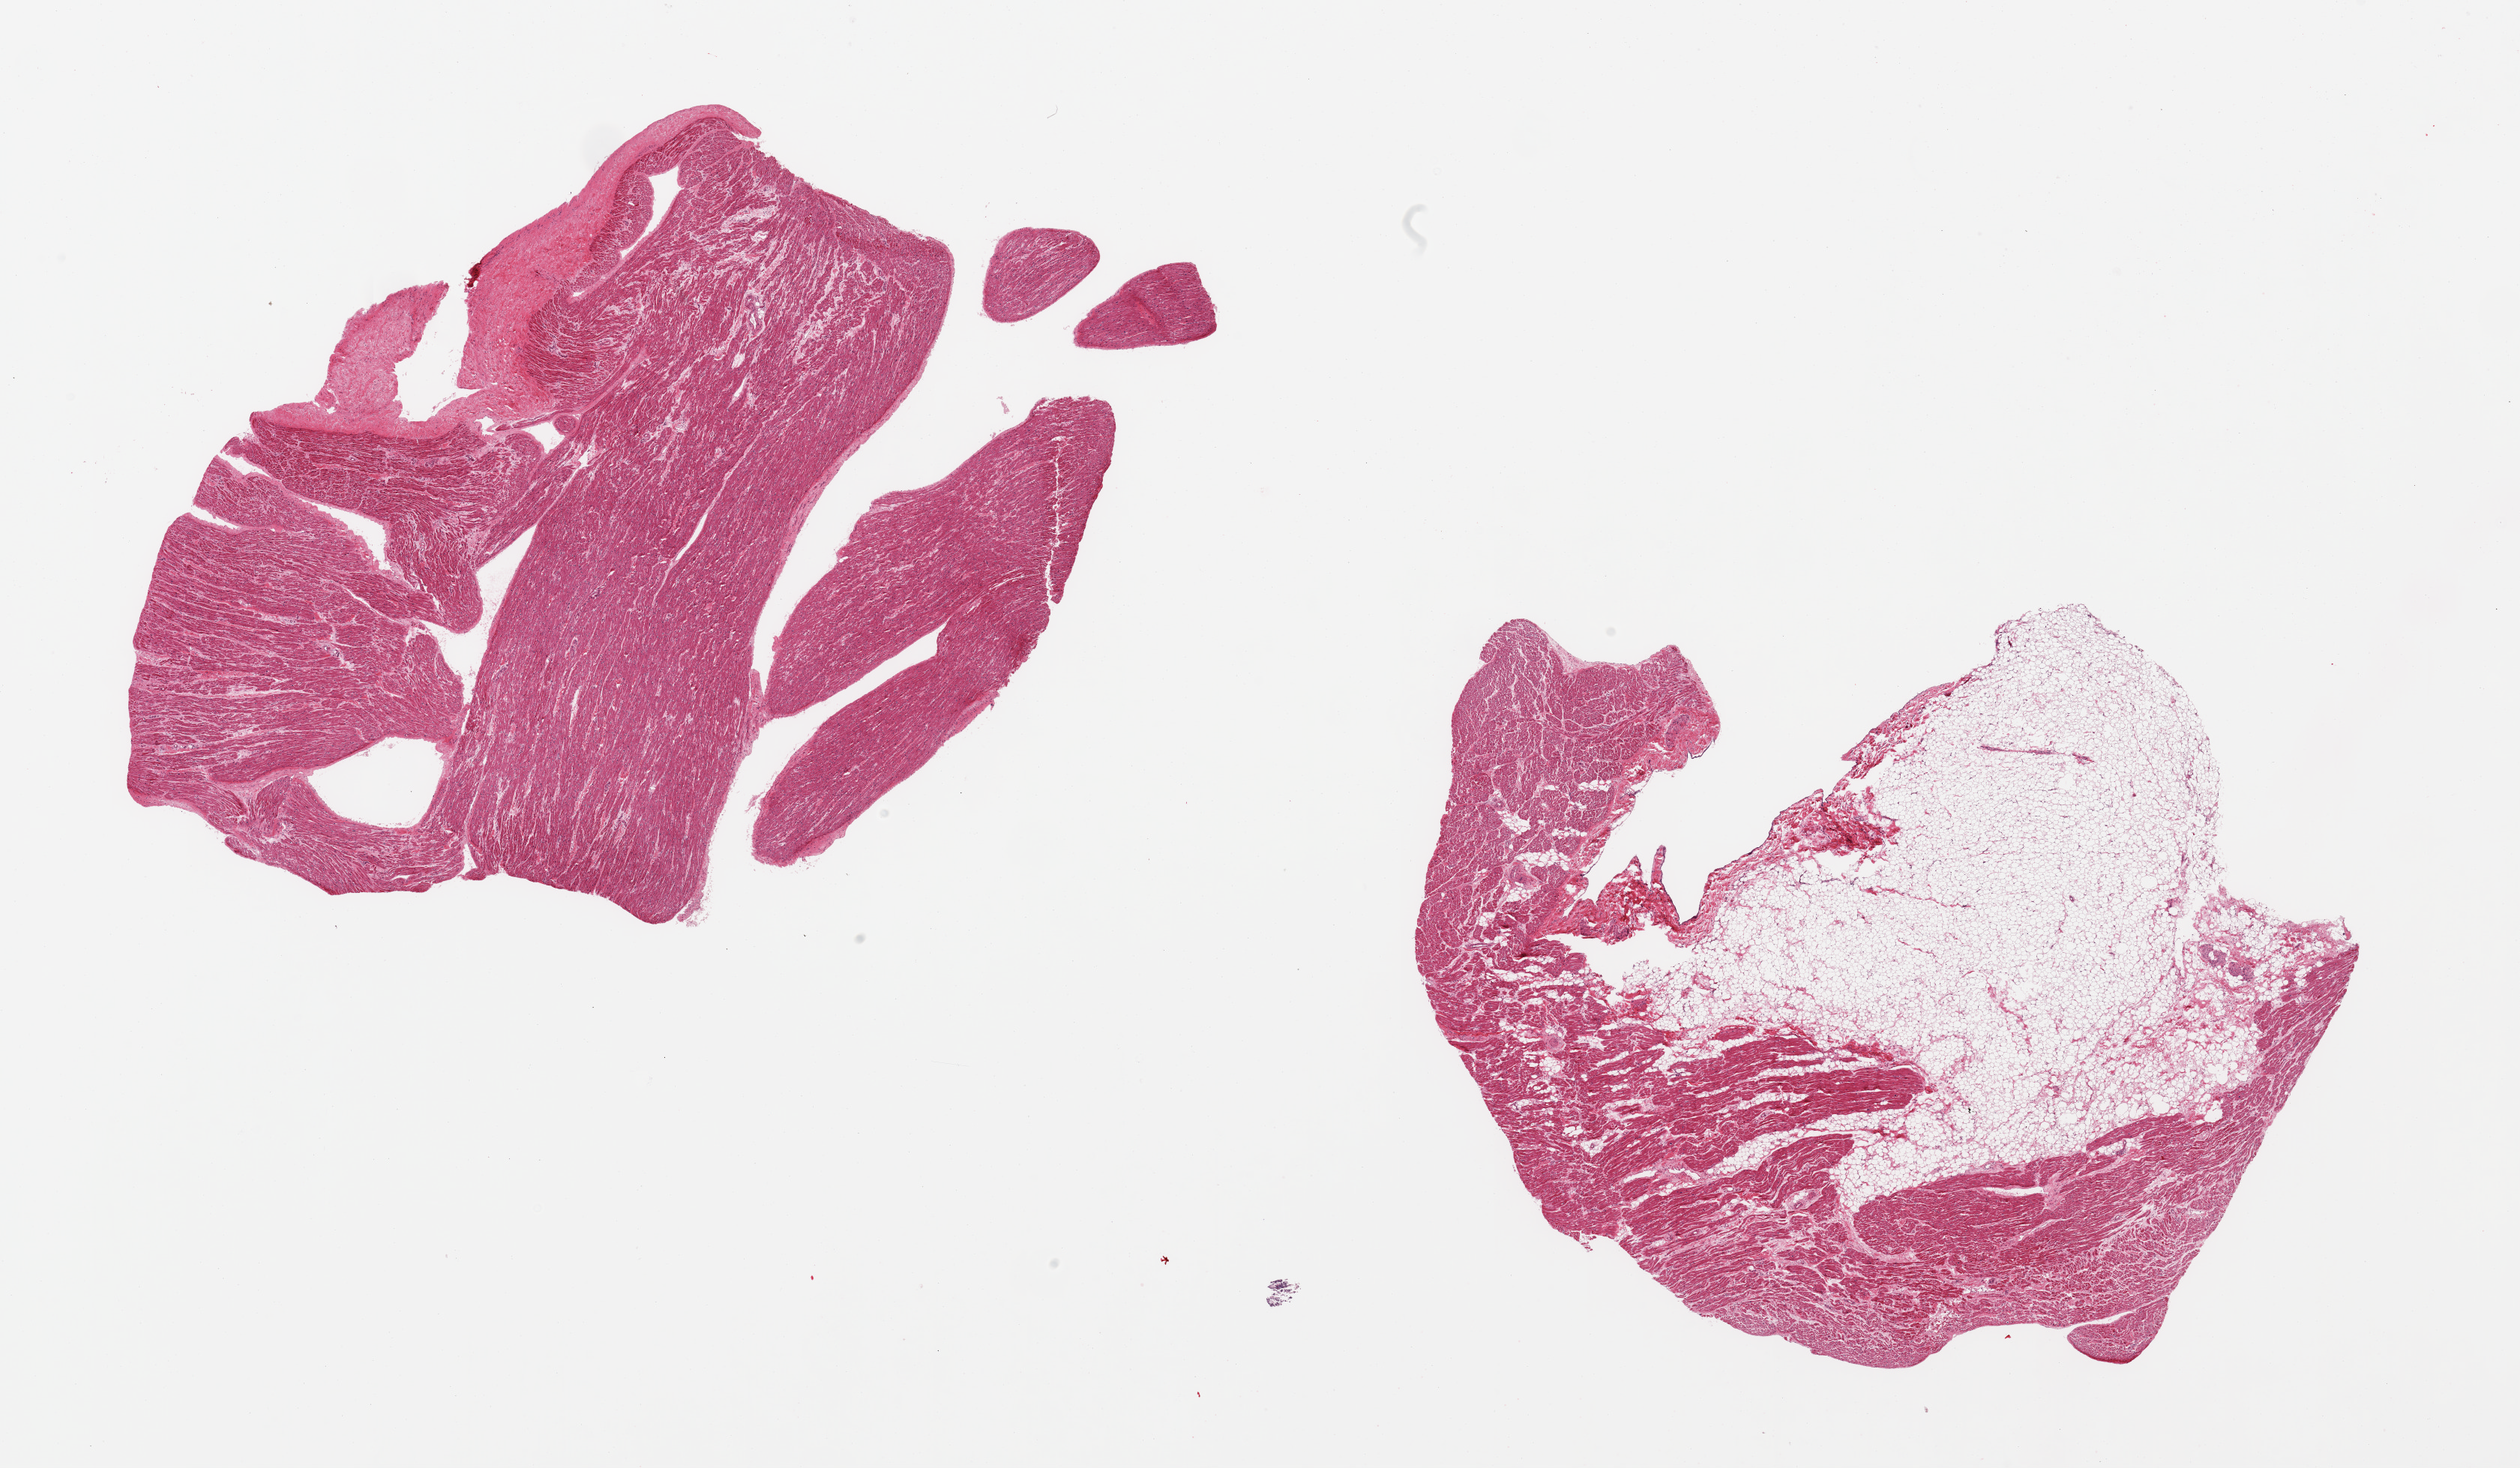
Digitized hematoxylin and eosin (H&E)-stained section, brightfield, a low-resolution overview of the entire scanned area, about 26.6 x 15.5 mm; PAXgene-fixed paraffin-embedded (PFPE) section; sampled site (target tissue): auricular appendage; tissue donor sample.
Review note (as recorded): 2 pieces; 1 piece has 10% fibrous content on edge and no fat; other has 50% fat.